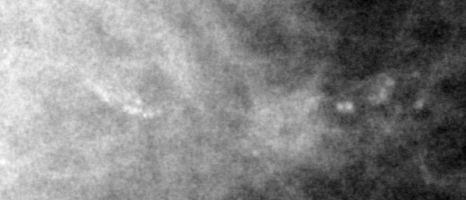
Crop from a digitized film mammogram around one marked abnormality; right breast; MLO view; BI-RADS breast density category 2 (scale 1–4).
Calcifications, morphology pleomorphic, distribution linear; BI-RADS assessment category 4; subtlety rating 2 on a 1 (subtle) to 5 (obvious) scale; pathology result (as recorded, not read from the image): malignant.